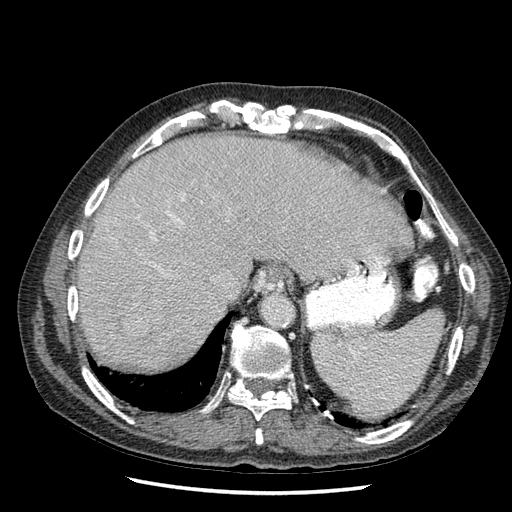
Contrast-enhanced abdominal CT (liver protocol), one axial slice; position 45 of 67 along the scan axis; 120 kVp; soft-tissue window (W 400 / L 40 HU); 2.5 mm slice thickness; 512 × 512 image matrix. From the clinical record (not read from this slice): diagnosis: hepatocellular carcinoma (patient treated with transarterial chemoembolisation; whether this scan precedes or follows treatment is not stated here); TNM stage (as recorded): Stage-I; Child-Pugh class: A; tumour differentiation: moderately differentiated; tumour nodularity: uninodular.
Annotated regions visible in this slice (semi-automatically segmented with operator editing):
- liver parenchyma outside the tumour (the mass and vessels are separate outlines, so this box may not span the whole liver): bounding box <78,133,412,376> (left, top, right, bottom; pixels)
- mass: <106,294,163,340>
- liver vessels: <114,181,221,274>